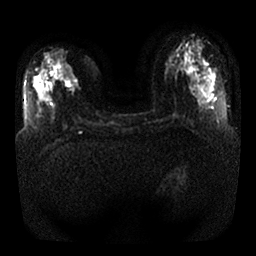
Breast MRI, one axial slice. Position 11 of 32 along the scan axis. Diffusion-weighted series; image 2 of 4 stored at this slice position (different b-values; order by instance number). 1.5 T. 4 mm slice thickness. 256 × 256 image matrix. Female patient.
Structures marked on this image (expert manual segmentation):
- tumour on diffusion-weighted imaging: box from (x=64, y=69) to (x=77, y=87) px